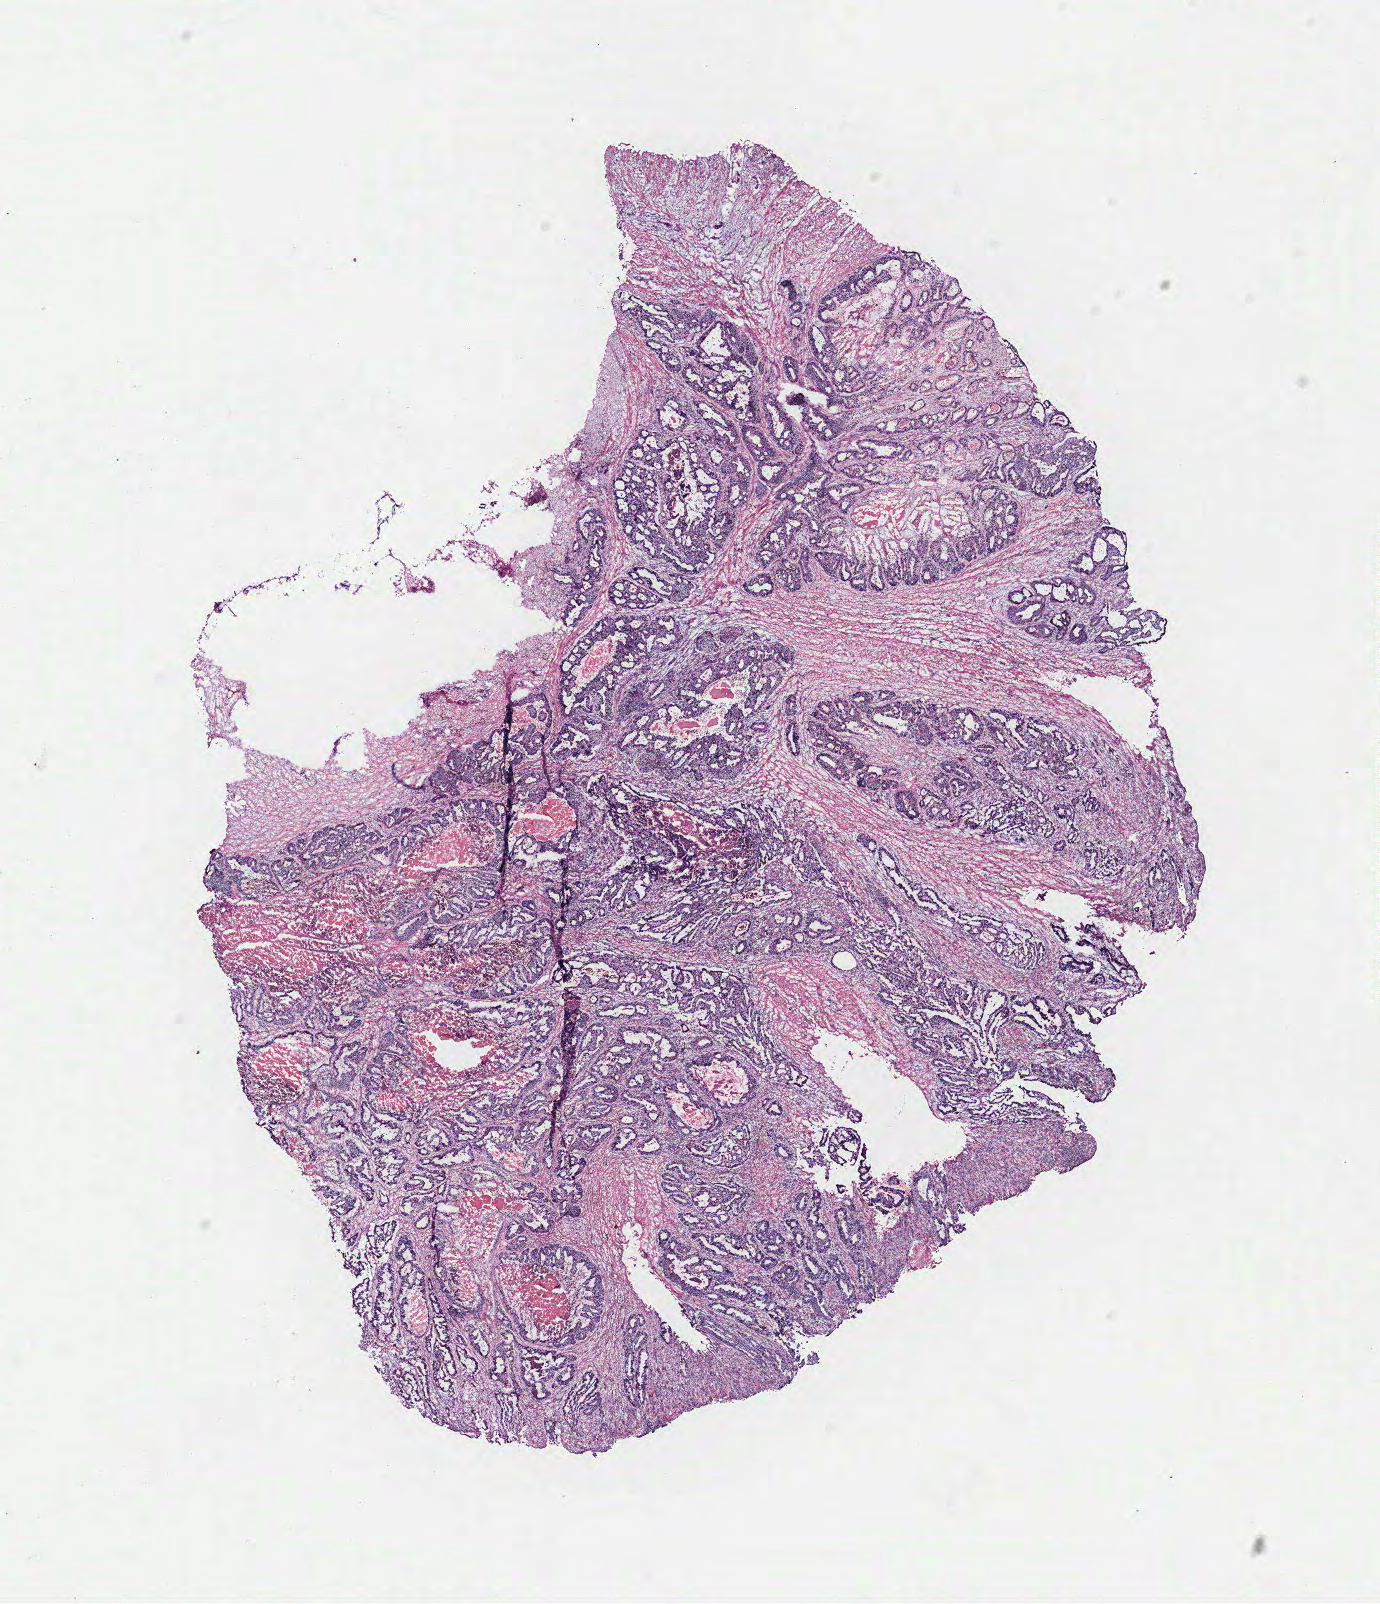
Whole-slide histology image, Hematoxylin and eosin (H&E) stained — whole scanned area (about 11.0 x 12.8 mm) shown as a low-resolution overview. Colon, normal (non-tumour) tissue. Patient: female, age 64 years.
This section: normal (non-tumour) tissue from the same patient. Patient diagnosis: Adenocarcinoma, NOS.